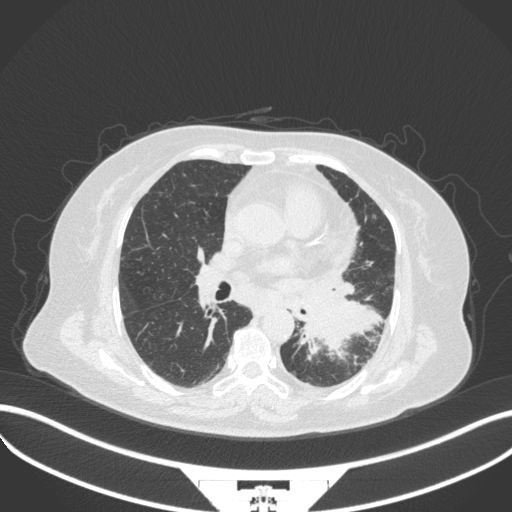
Chest CT, one axial slice; position 180 of 328 along the scan axis; 120 kVp; lung window (W 1500 / L -600 HU); 1 mm slice thickness; 512 × 512 image matrix. Patient: female, 69 years. Case-level facts recorded for this patient, not image findings: clinical TNM (as recorded): T2b N3 M1.
Annotated regions visible in this slice (rectangle marked by the reading radiologist):
- lung tumour (recorded histology: adenocarcinoma): bounding box <295,289,383,365> (left, top, right, bottom; pixels)